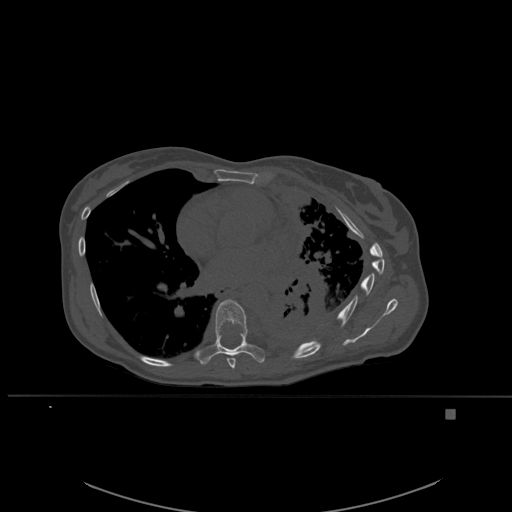
CT including the spine, one axial slice. Position 353 of 537 along the scan axis. Bone window (W 1800 / L 400 HU). 1.5 mm slice thickness. 512 × 512 image matrix, field of view 440 × 440 mm. Patient: female, 45 years. Case-level facts recorded for this patient, not image findings: primary cancer: lung.
Structures marked on this image (semi-automatically segmented with operator editing):
- T7 vertebra: bounding box [x1, y1, x2, y2] px = [226, 358, 236, 369]
- T8 vertebra: [196, 299, 265, 365]